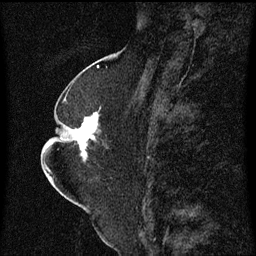
Breast MRI (dynamic contrast-enhanced), one sagittal slice. Position 29 of 60 along the scan axis. Dynamic contrast-enhanced series, image 2 of 3 at this slice position (ordered by acquisition). 1.5 T. TE 4.2 ms, TR 8.4 ms. 2 mm slice thickness. 256 × 256 image matrix, field of view 200 × 200 mm. Patient: female, 52 years. From the clinical record (not read from this slice): setting: breast cancer imaged before/during neoadjuvant chemotherapy; receptor status: HR-positive, HER2-negative.
Outlined on this slice (semi-automatic segmentation, software-assisted and operator-edited):
- analysis volume of interest (the breast-tissue region the enhancement analysis was run in; not a lesion): bounding box [x1, y1, x2, y2] px = [64, 108, 109, 163]
- tumour enhancement mask (voxels above the 70 % enhancement threshold inside the analysis volume of interest): [76, 114, 98, 161]